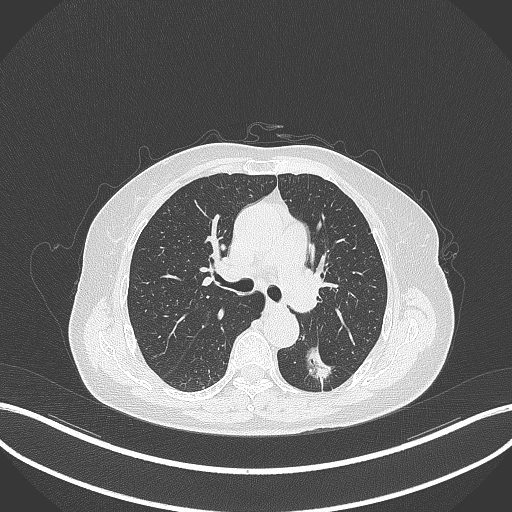
Chest CT, one axial slice. Position 187 of 352 along the scan axis. Lung window (W 1500 / L -600 HU). 1 mm slice thickness. 512 × 512 image matrix, field of view 400 × 400 mm. Patient: female, 70 years. Case-level facts recorded for this patient, not image findings: clinical TNM (as recorded): T1c N0 M0.
Structures marked on this image (rectangle marked by the reading radiologist):
- lung tumour (recorded histology: adenocarcinoma): bounding box <297,333,337,387> (left, top, right, bottom; pixels)